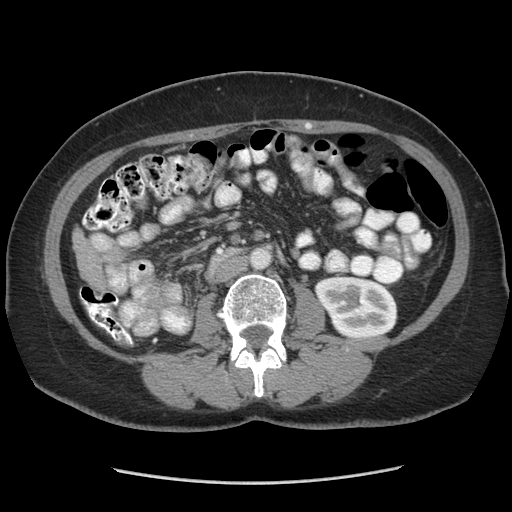
Contrast-enhanced abdominal CT (liver protocol), one axial slice. Position 110 of 185 along the scan axis. Reconstruction kernel STANDARD. Soft-tissue window (W 400 / L 40 HU). 2.5 mm slice thickness. 512 × 512 image matrix, field of view 360 × 360 mm. Case-level facts recorded for this patient, not image findings: diagnosis: hepatocellular carcinoma (patient treated with transarterial chemoembolisation; whether this scan precedes or follows treatment is not stated here); TNM stage (as recorded): Stage-I; Child-Pugh class: A; tumour nodularity: uninodular.
Structures marked on this image (semi-automatically segmented with operator editing):
- liver parenchyma outside the tumour (the mass and vessels are separate outlines, so this box may not span the whole liver): bounding box (x1, y1, x2, y2) in pixels: (72, 229, 102, 284)